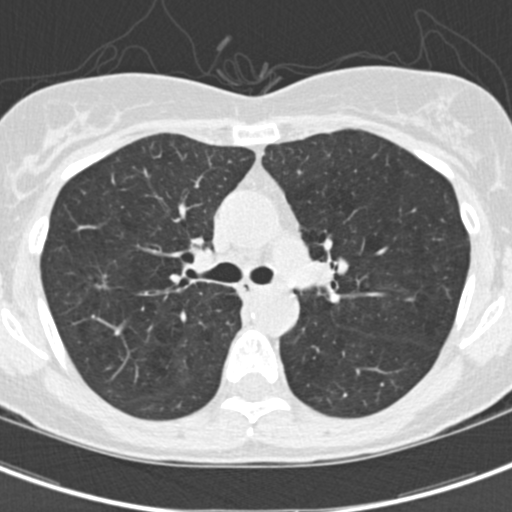
Low-dose screening chest CT, one axial slice; slice 101 of 154 in the series (ordered by position); 120 kVp; lung window (W 1500 / L -600 HU); 2 mm slice thickness; 512 × 512 image matrix, field of view 280 × 280 mm.
Structures marked on this image (outlined manually by an expert reader):
- lesion 1 (tumor, upper lobe of right lung): bounding box (x1, y1, x2, y2) in pixels: (94, 272, 108, 291)